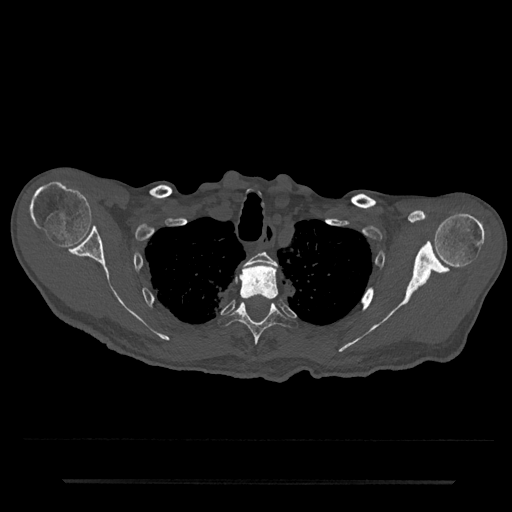
CT including the spine, one axial slice. Slice 642 of 797 in the series (ordered by position). Reconstruction kernel Br40s/3. 120 kVp. Bone window (W 1800 / L 400 HU). 0.5 mm slice thickness. 512 × 512 image matrix. Patient: male, 74 years. From the clinical record (not read from this slice): primary cancer: prostate.
Structures marked on this image (semi-automatic segmentation, software-assisted and operator-edited):
- T2 vertebra: bounding box <244,252,277,268> (left, top, right, bottom; pixels)
- T3 vertebra: <240,264,279,300>
- T4 vertebra: <219,298,297,359>